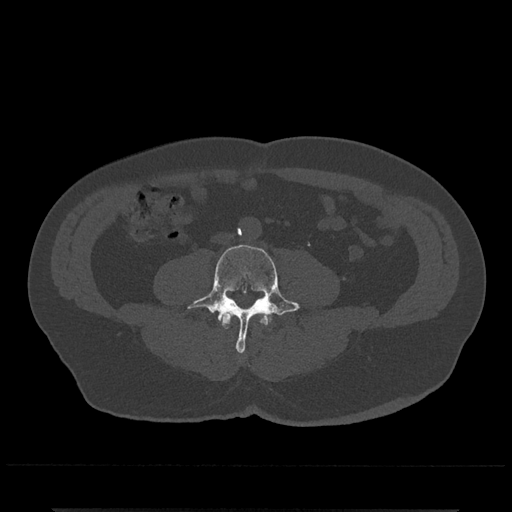
CT including the spine, one axial slice; slice 158 of 797 in the series (ordered by position); 120 kVp; bone window (W 1800 / L 400 HU); 0.5 mm slice thickness; 512 × 512 image matrix, field of view 393 × 393 mm. Patient: male, 67 years. From the clinical record (not read from this slice): primary cancer: prostate.
Outlined on this slice (semi-automatic segmentation, software-assisted and operator-edited):
- L3 vertebra: bounding box [x1, y1, x2, y2] px = [220, 311, 271, 328]
- L4 vertebra: [188, 244, 300, 353]